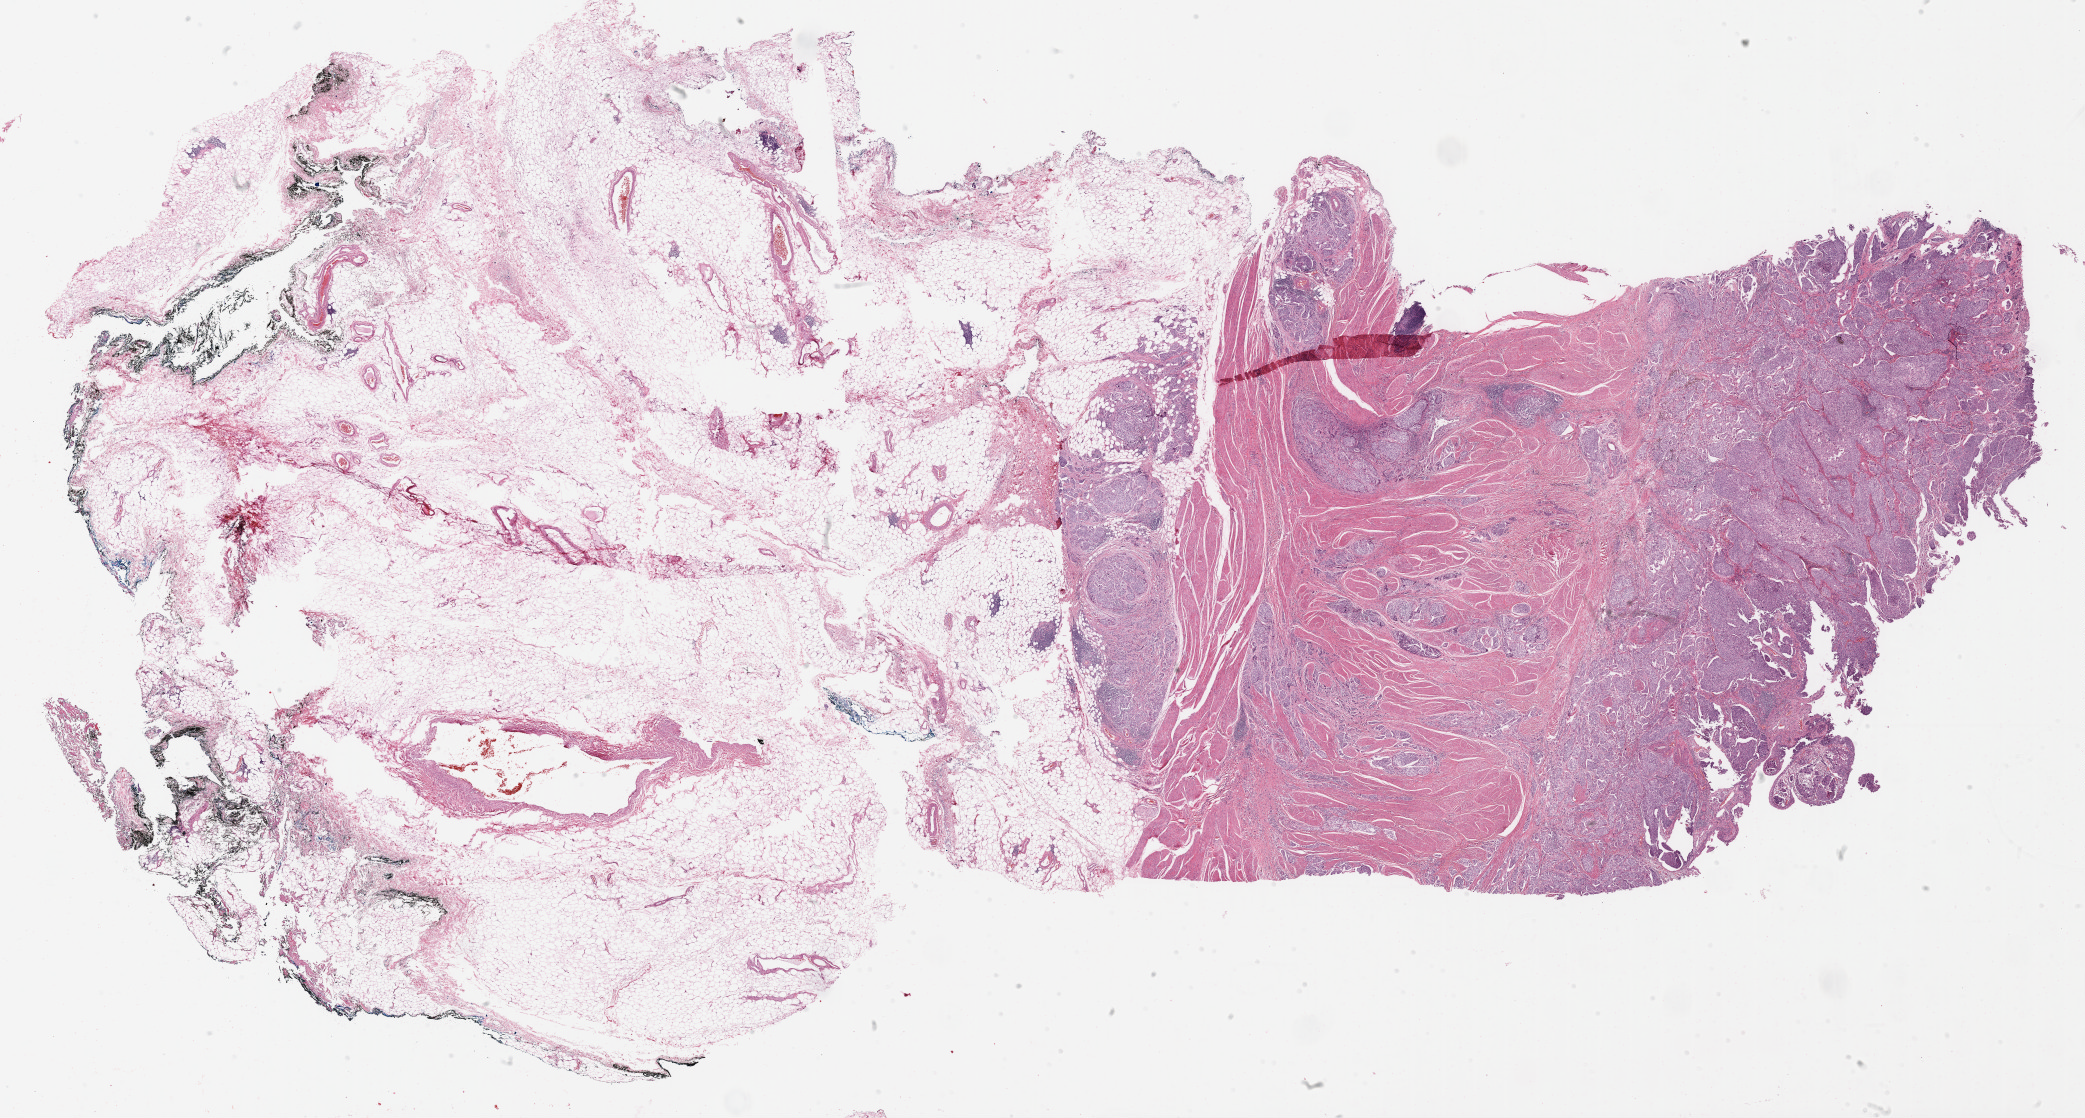
Whole-slide histology image, H&E, shown as a low-resolution overview of the whole scanned area (about 33.7 x 18.1 mm, from a 40x scan), formalin-fixed paraffin-embedded (FFPE) diagnostic section, bladder, primary tumour sample. Male, age 56 years at initial diagnosis.
Pathologic diagnosis: Transitional cell carcinoma (anterior wall of bladder).